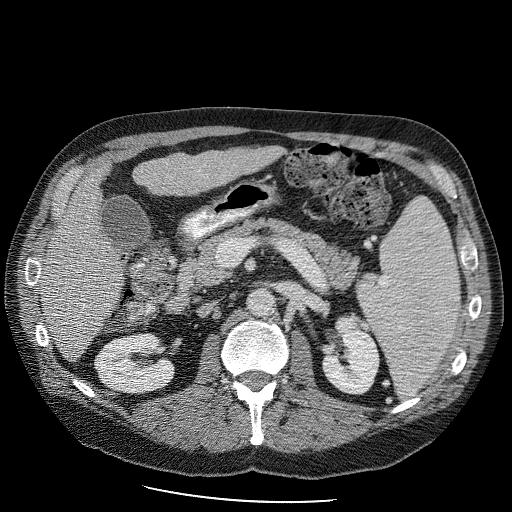
Contrast-enhanced abdominal CT (liver protocol), one axial slice. Position 38 of 98 along the scan axis. Reconstruction kernel STANDARD. 120 kVp. Soft-tissue window (W 400 / L 40 HU). 2.5 mm slice thickness. 512 × 512 image matrix, field of view 400 × 400 mm. Case-level facts recorded for this patient, not image findings: diagnosis: hepatocellular carcinoma (patient treated with transarterial chemoembolisation; whether this scan precedes or follows treatment is not stated here); TNM stage (as recorded): Stage-II; Child-Pugh class: B.
Structures marked on this image (semi-automatic segmentation, software-assisted and operator-edited):
- liver parenchyma outside the tumour (the mass and vessels are separate outlines, so this box may not span the whole liver): bounding box <40,142,287,360> (left, top, right, bottom; pixels)